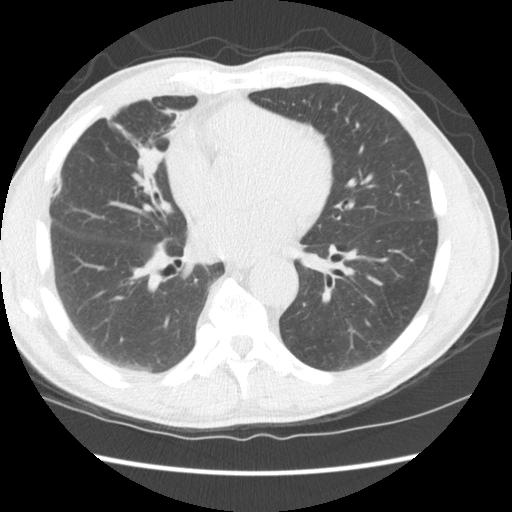
Chest CT (low-dose screening protocol), one axial image. Third annual screen. Lung window (W 1500 / L -600 HU). Standard (soft-tissue) reconstruction kernel (STANDARD). 120 kVp. Slice 65 of 147 in the series. Male participant, aged 65 years at enrolment.
- Lesion marked by an expert reader, bounding box <105,131,173,209> (left, top, right, bottom; pixels).
- The exam's reader record, not a measurement of the box and not confirmed to be the same lesion: non-calcified nodule or mass ≥4 mm, right middle lobe, 16 × 15 mm, smooth margins, soft tissue attenuation, pre-existing on the prior screen: yes; interval growth: yes.
- Participant outcome: lung cancer diagnosed 357 days after this screen — squamous cell carcinoma, NOS, right middle lobe, poorly differentiated (G3), stage IA (AJCC 6th edition), 23 mm at pathology.